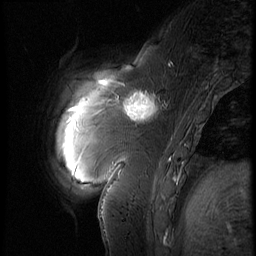
Breast MRI (dynamic contrast-enhanced), one sagittal slice; slice 15 of 60 in the series (ordered by position); 3 images stored at this slice position (order not interpretable as contrast timing); 1.5 T; TE 4.2 ms, TR 9 ms; 2.5 mm slice thickness; 256 × 256 image matrix, field of view 180 × 180 mm. Female patient, age 57 years. From the clinical record (not read from this slice): setting: breast cancer imaged before/during neoadjuvant chemotherapy; receptor status: triple-negative.
Structures marked on this image (semi-automatically segmented with operator editing):
- analysis volume of interest (the breast-tissue region the enhancement analysis was run in; not a lesion): bounding box [x1, y1, x2, y2] px = [114, 83, 170, 131]
- tumour enhancement mask (voxels above the 140 % enhancement threshold inside the analysis volume of interest): [123, 92, 158, 120]